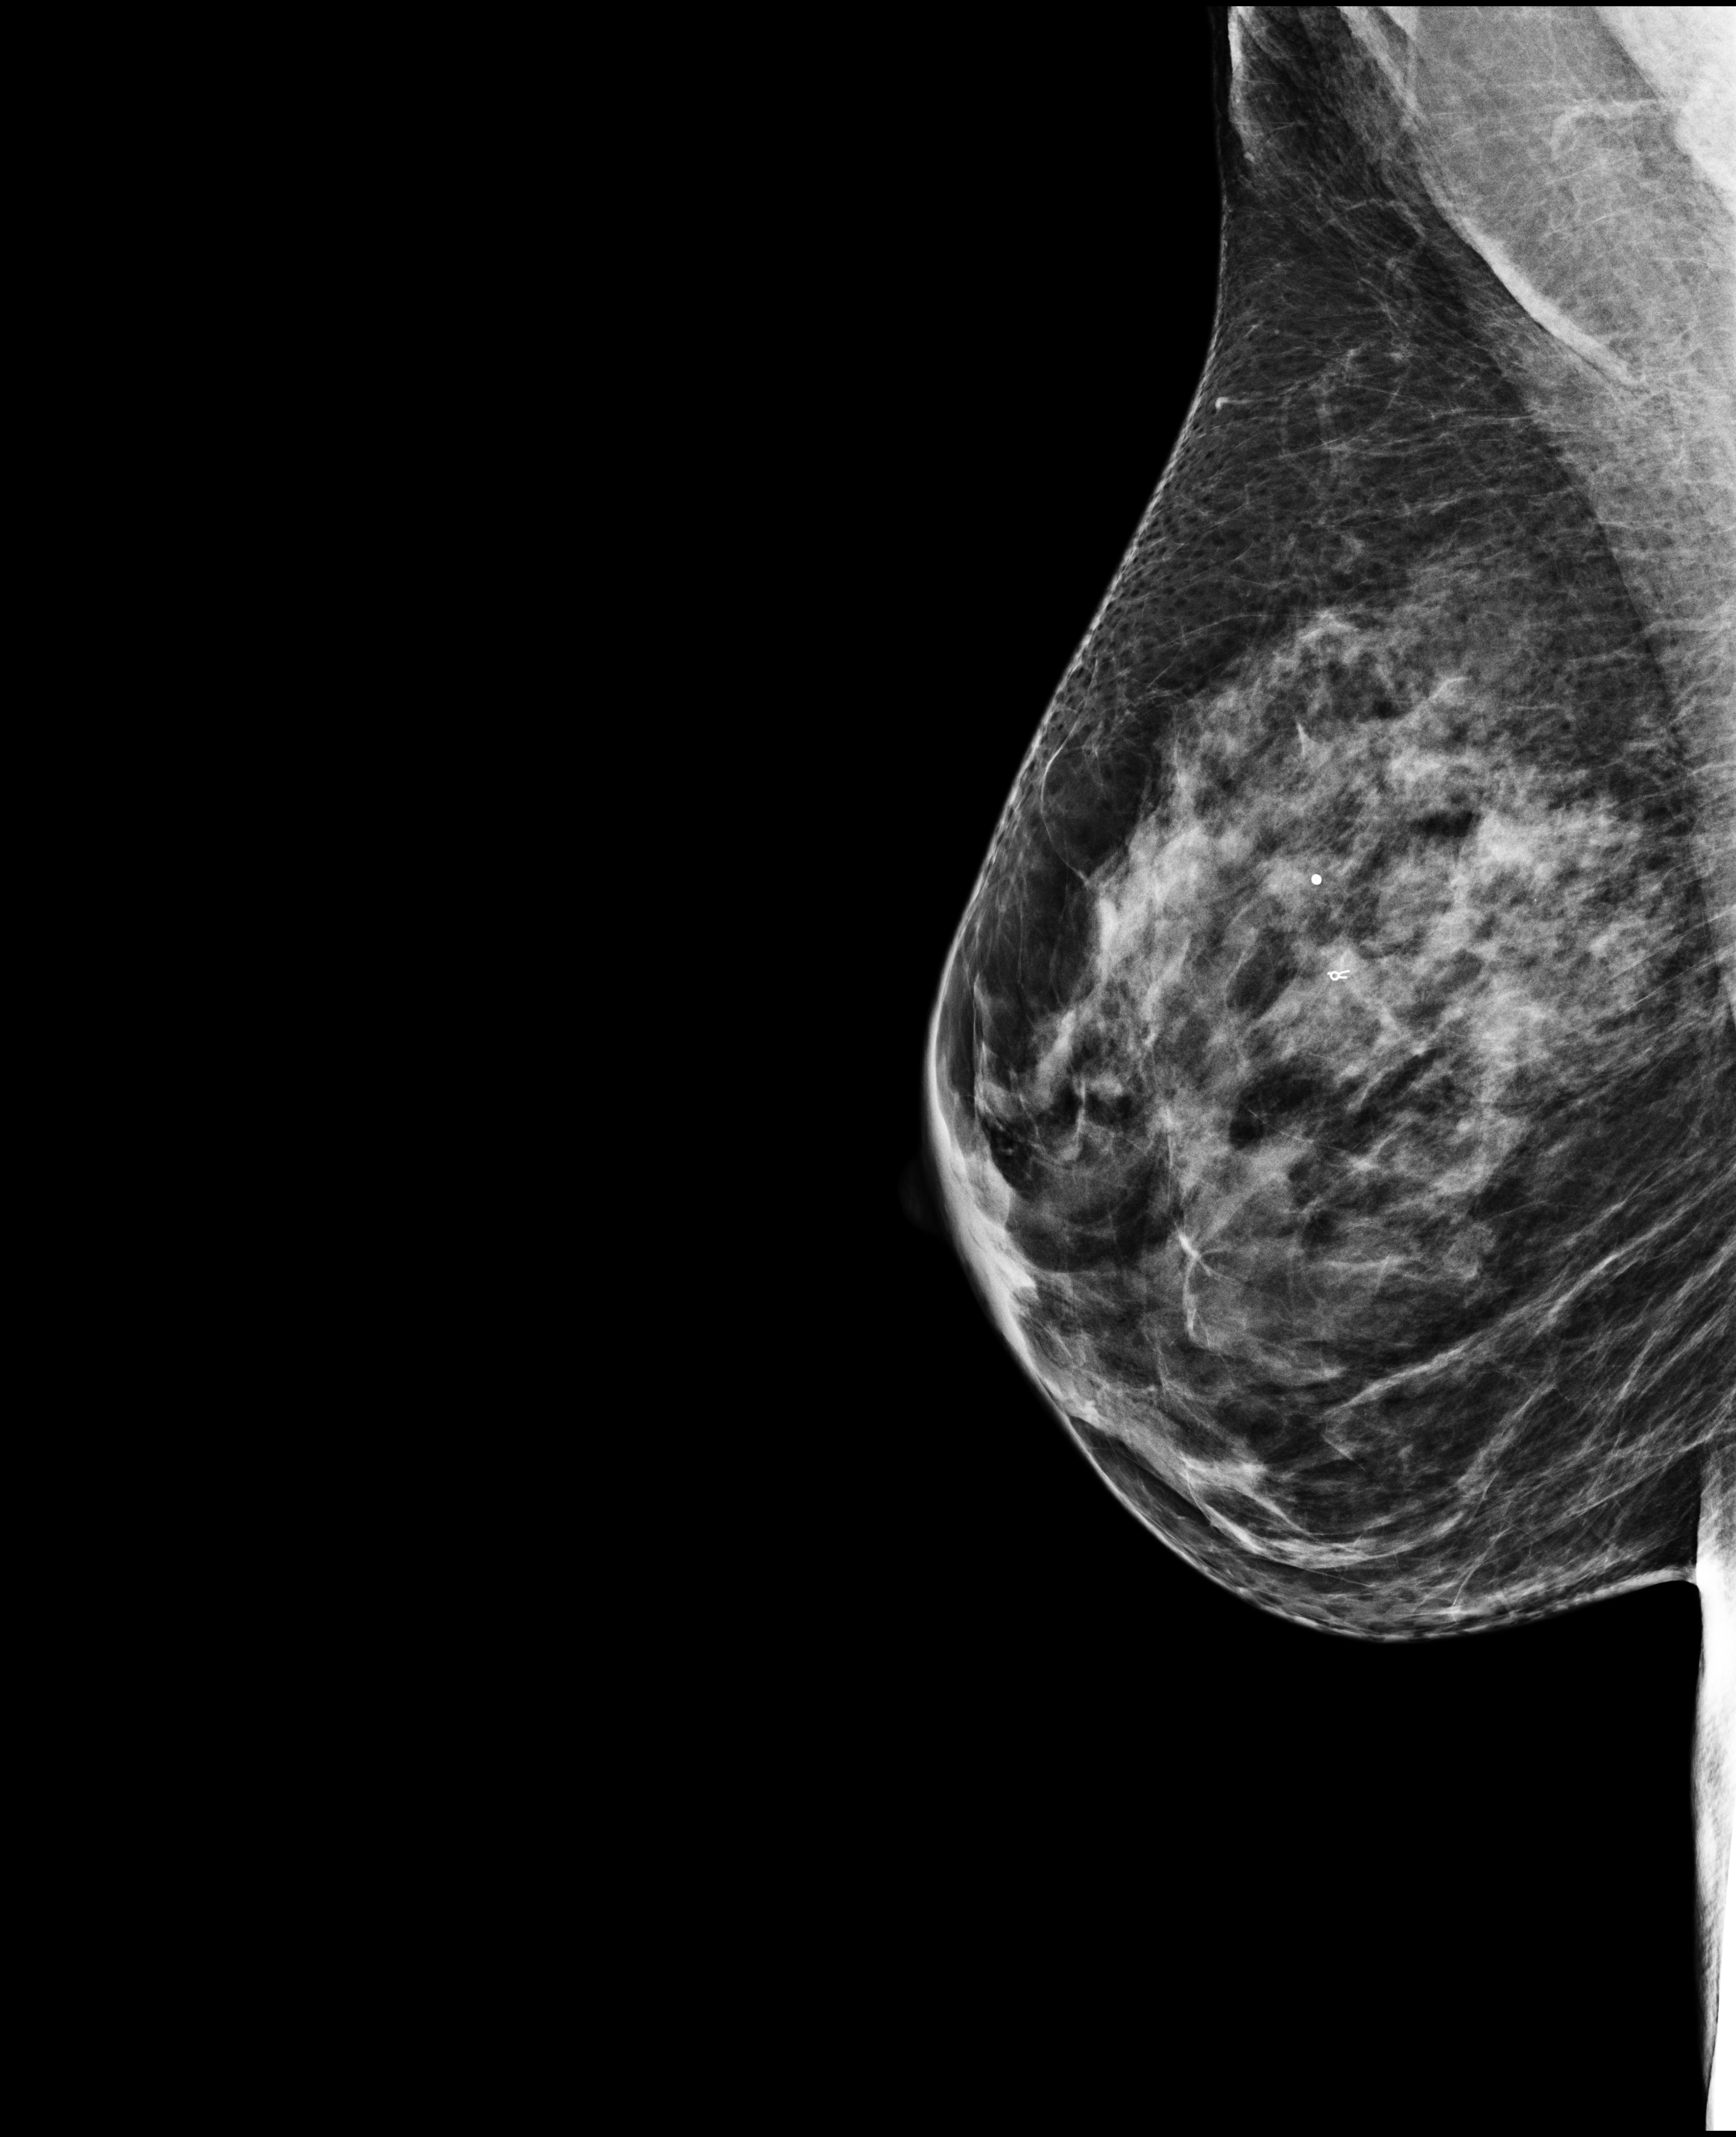
Annual screening mammography examination; system: Selenia Dimensions.
Image type: full-field digital mammogram. Breast: right. Projection: MLO view.